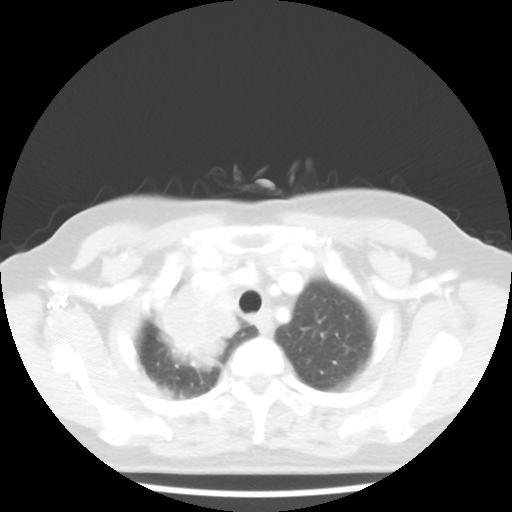
Chest CT, one axial slice; slice 38 of 44 in the series (ordered by position); lung window (W 1500 / L -600 HU); 5 mm slice thickness; 512 × 512 image matrix, field of view 316 × 316 mm. Female patient, age 62 years. Case-level facts recorded for this patient, not image findings: clinical TNM (as recorded): T3 N0 M0; histopathological grade: G3.
Structures marked on this image (rectangle marked by the reading radiologist):
- lung tumour (recorded histology: small cell carcinoma): box from (x=139, y=274) to (x=255, y=377) px